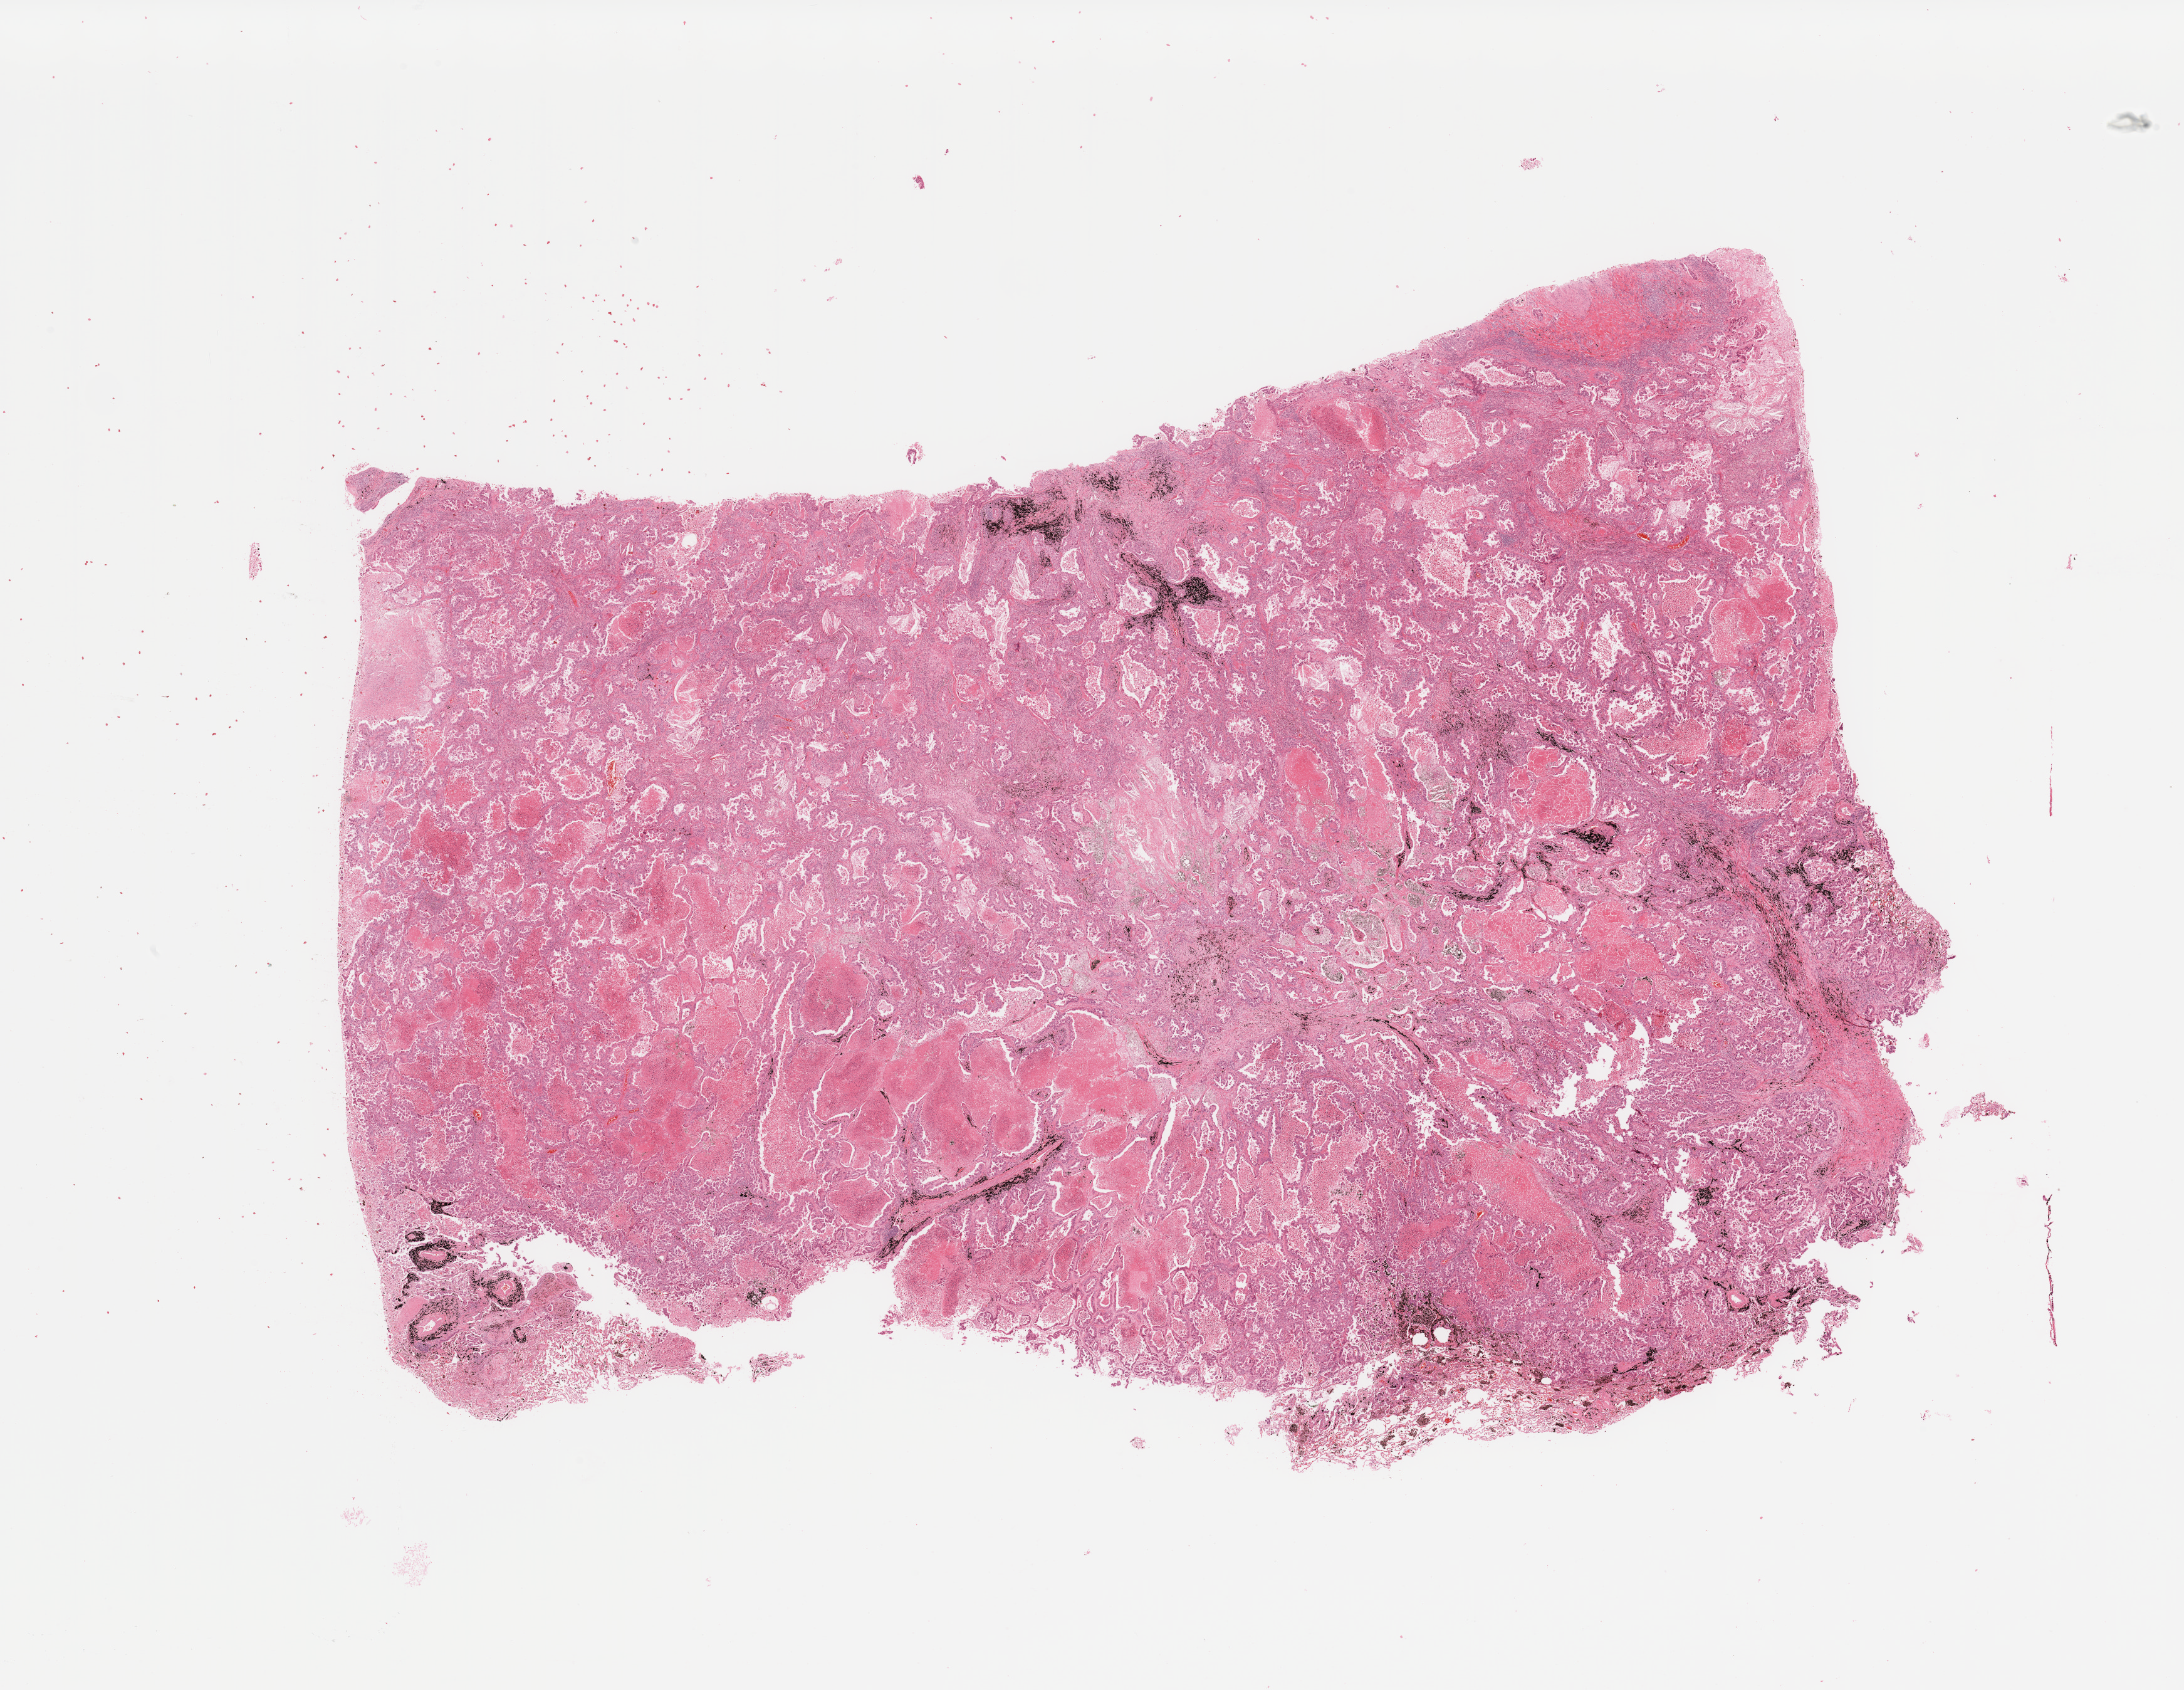
H&E-stained whole-slide image, a low-resolution overview of the entire scanned area, about 27.6 x 21.3 mm (acquisition: 20x scan). Lung, tumour tissue. Patient: male, age 57 years. Histologic grade: G2 (moderately differentiated).
AJCC pathologic stage: IIIA. Histologic diagnosis: Adenocarcinoma, NOS.